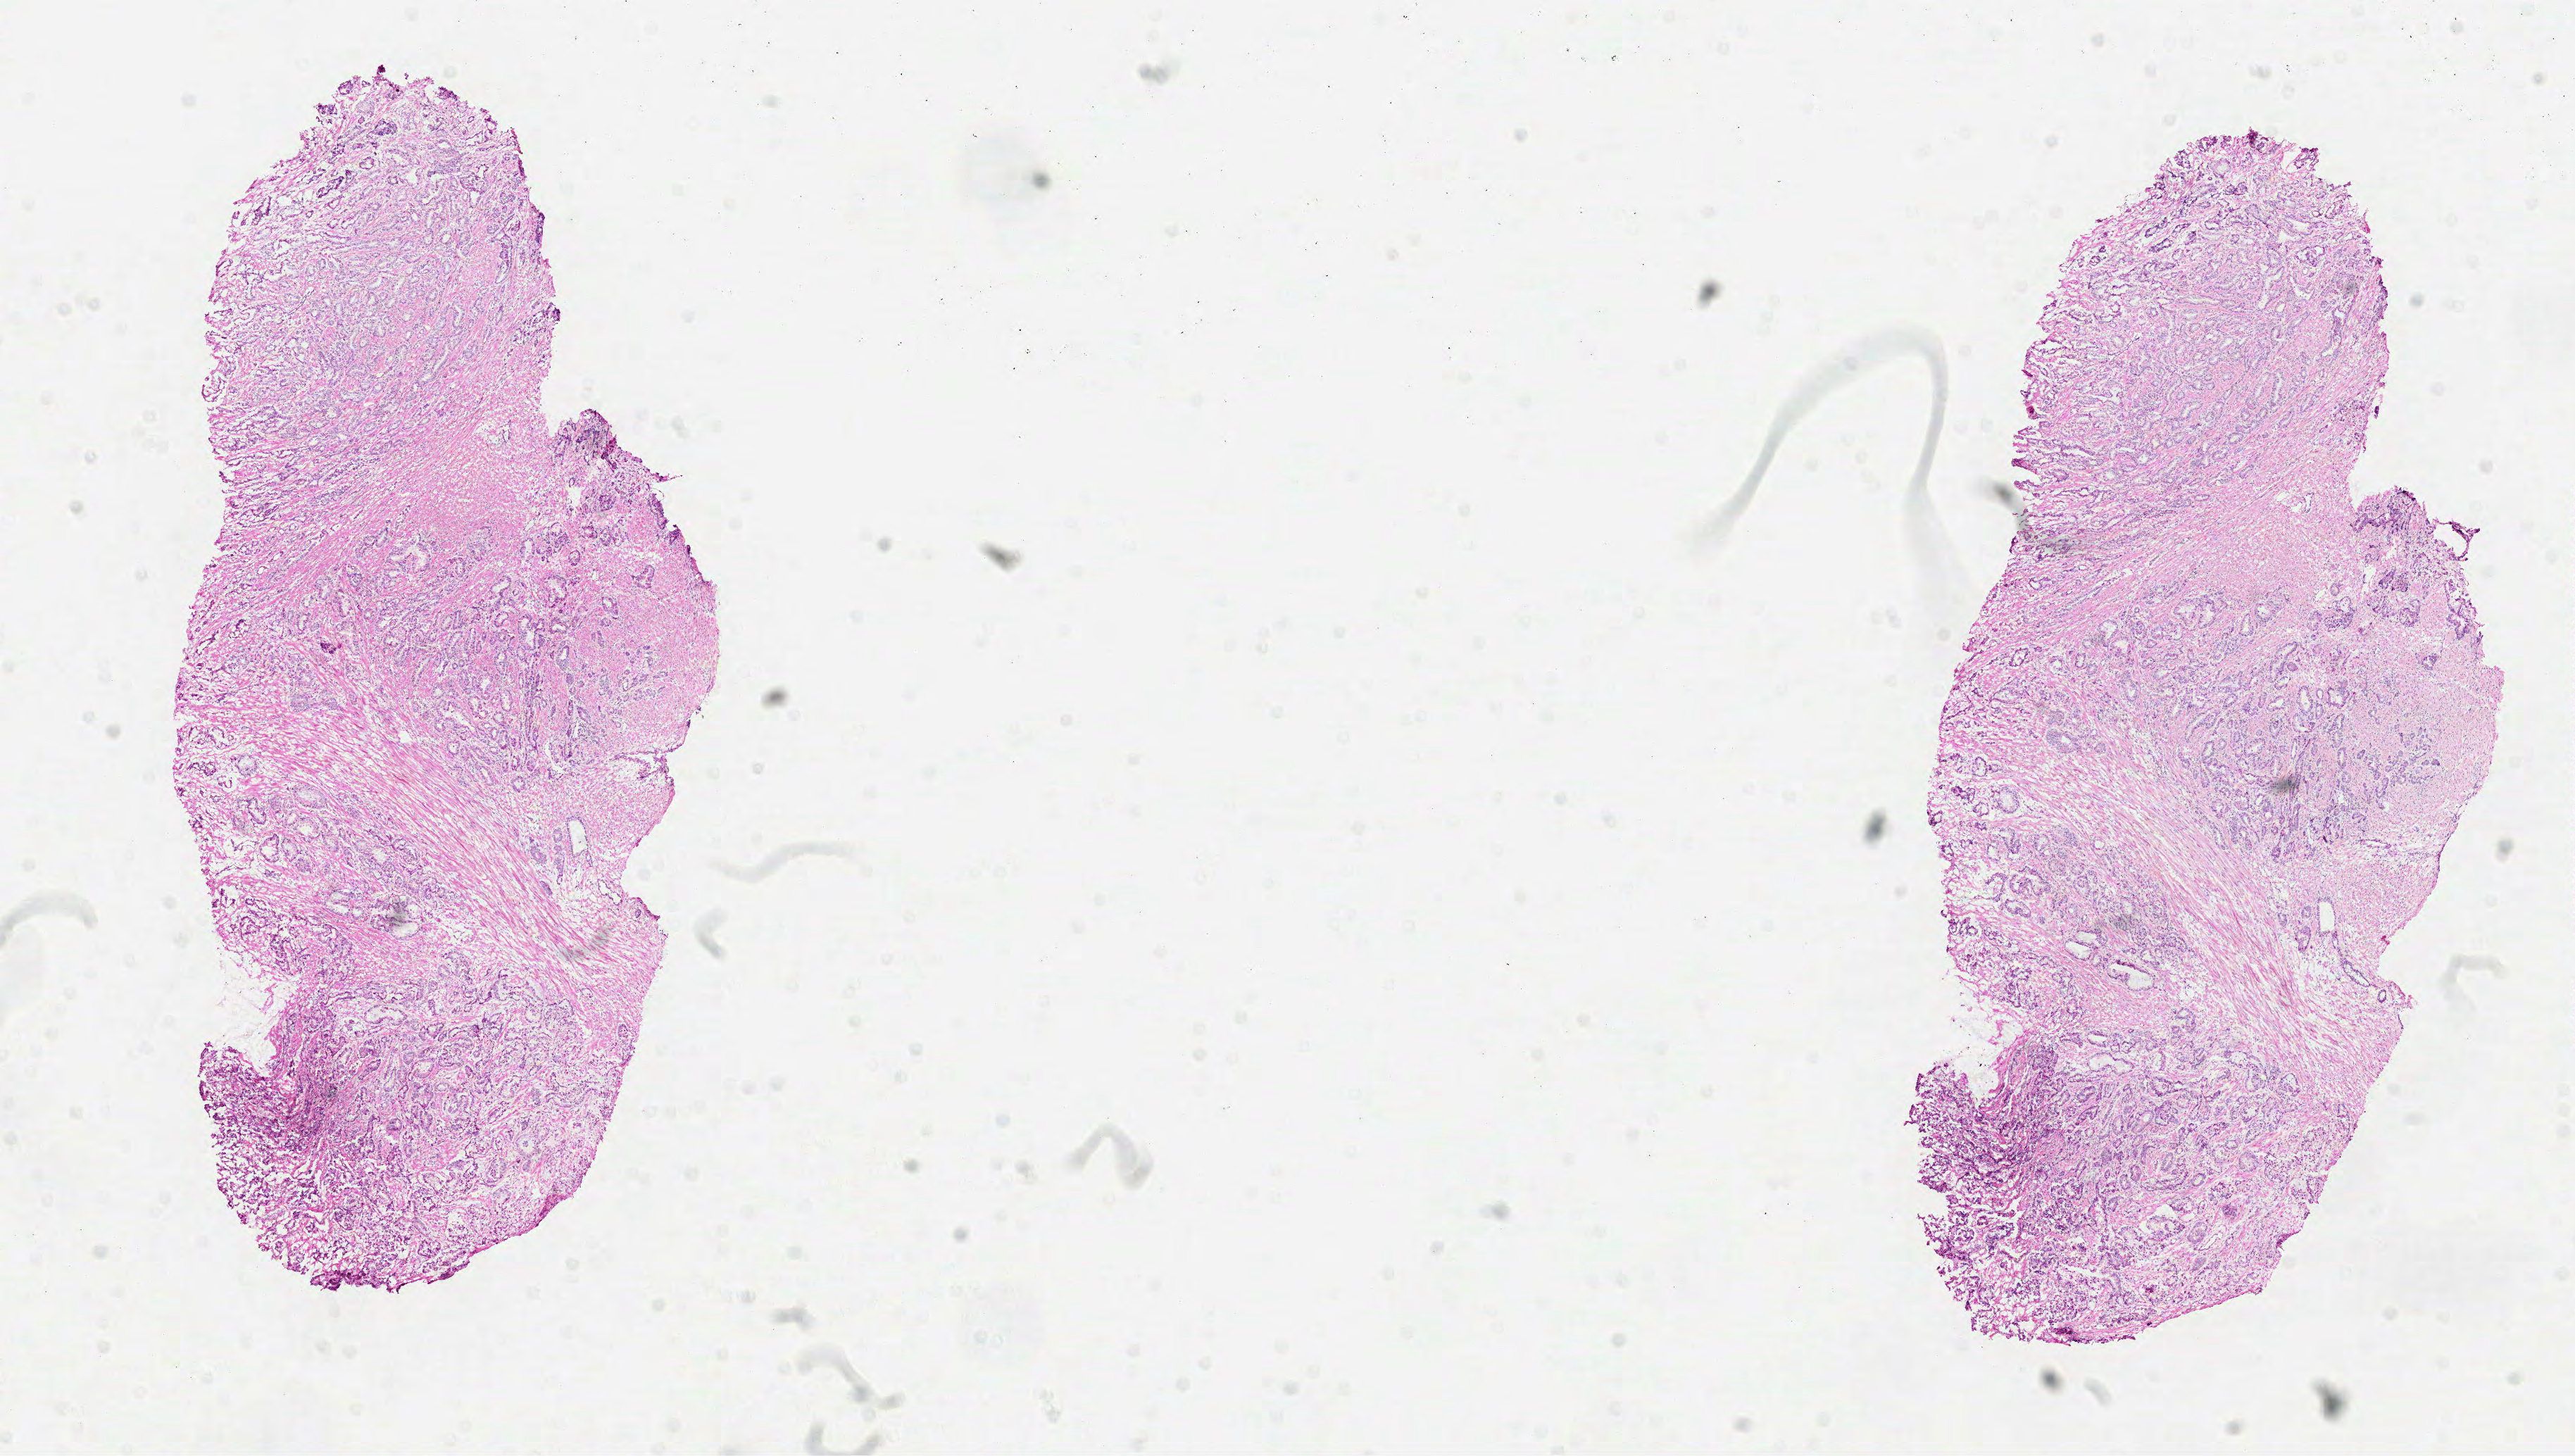
Digitized Hematoxylin and eosin (H&E) stained tissue section (whole slide), low-resolution overview of the scanned area, about 14.7 x 8.3 mm; formalin-fixed paraffin-embedded (FFPE) diagnostic section; prostate, primary tumour sample. Male, age 66 years at initial diagnosis.
Diagnosis: Acinar cell carcinoma (prostate gland).